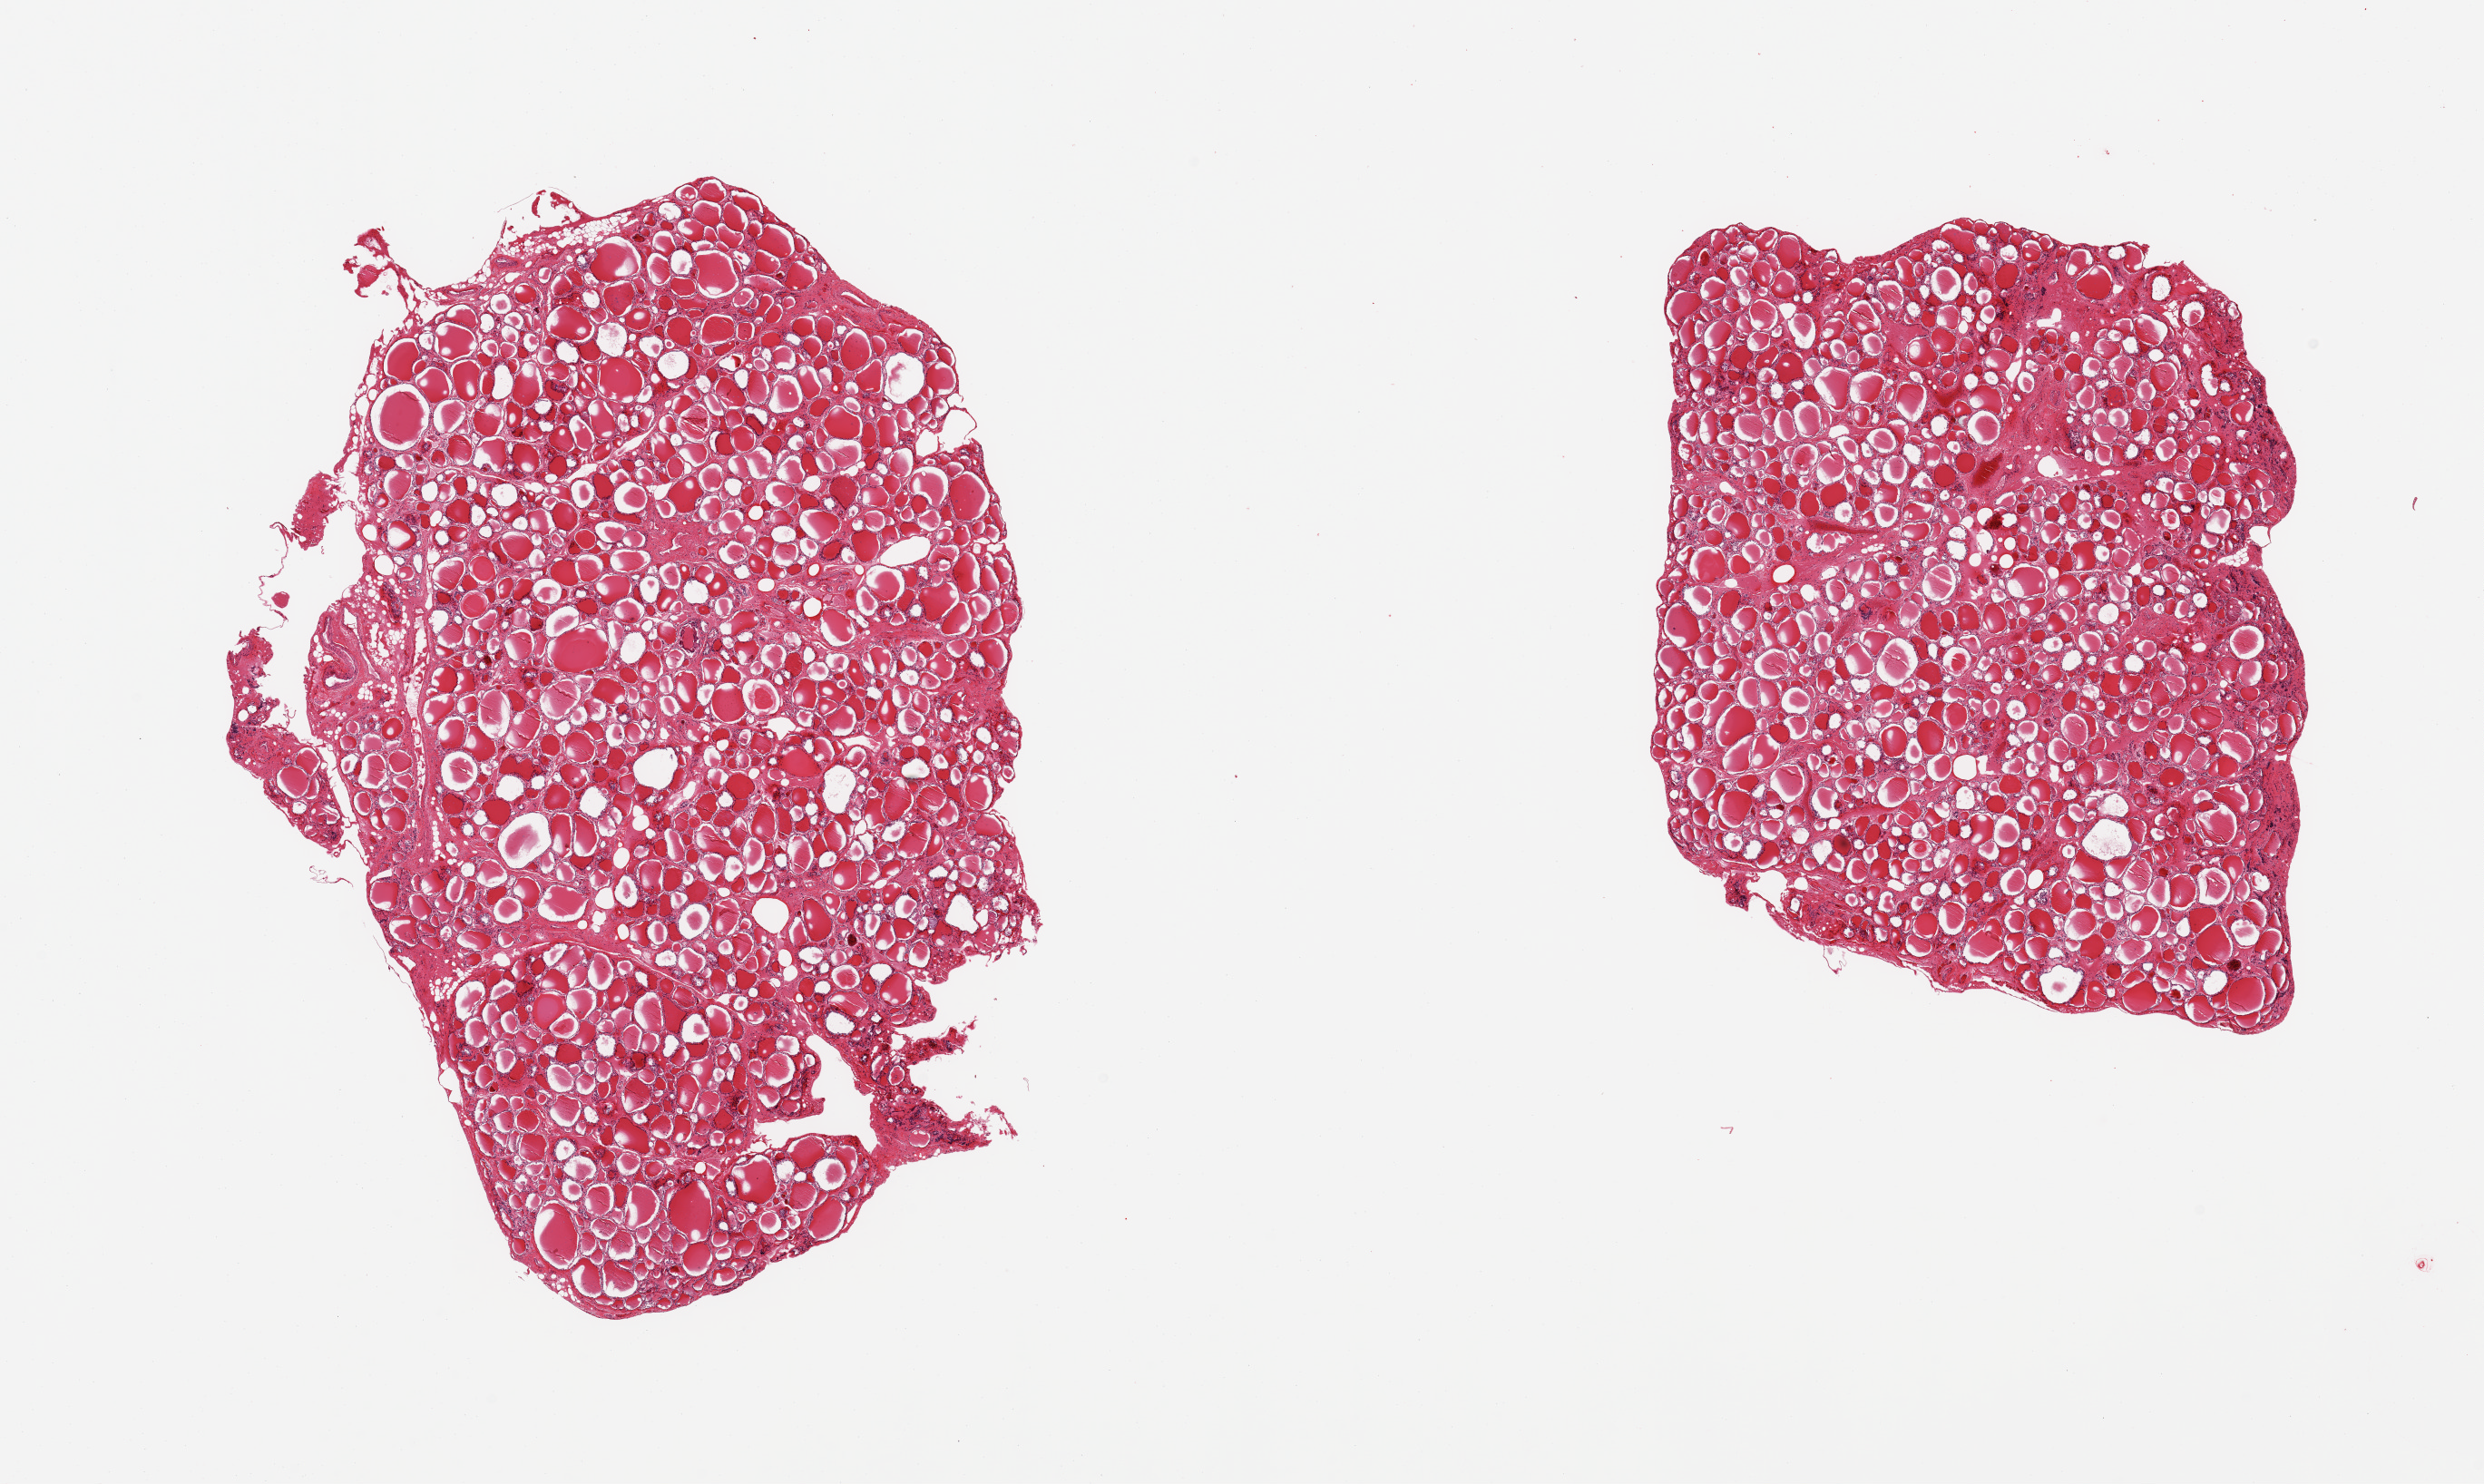
Haematoxylin and eosin whole-slide image, low-resolution overview of the scanned area, about 21.7 x 12.9 mm (acquisition: 20x scan); PAXgene-fixed paraffin-embedded (PFPE) section; section of thyroid (target tissue); donor tissue sample. Donor sex: male.
Pathologist's review note for this sample: 2 pieces, no abnormalities.